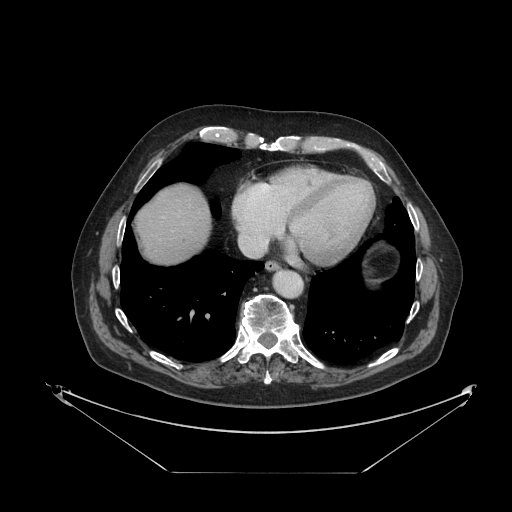
Contrast-enhanced abdominal CT, one axial slice. Slice 116 of 121 in the series (ordered by position). Reconstruction kernel STANDARD. 120 kVp. Intravenous contrast given. Soft-tissue window (W 400 / L 40 HU). 512 × 512 image matrix, field of view 500 × 500 mm. Male patient, age 68 years. From the clinical record (not read from this slice): diagnosis: colorectal cancer liver metastases, imaged before liver resection; multiple liver metastases: no; largest metastasis: 4 cm; disease in both lobes: no.
Annotated regions visible in this slice (expert manual segmentation):
- liver: bounding box [x1, y1, x2, y2] px = [137, 186, 210, 265]
- planned liver remnant (the part of the liver to remain after resection): [137, 186, 210, 265]